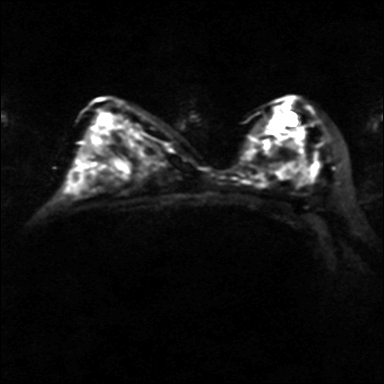
Breast MRI, one axial slice. Slice 23 of 40 in the series (ordered by position). Diffusion-weighted series; image 2 of 4 stored at this slice position (different b-values; order by instance number). 3 T. 4 mm slice thickness. 384 × 384 image matrix, field of view 320 × 320 mm. Female patient.
Outlined on this slice (expert manual segmentation):
- tumour on diffusion-weighted imaging: box from (x=263, y=126) to (x=304, y=148) px